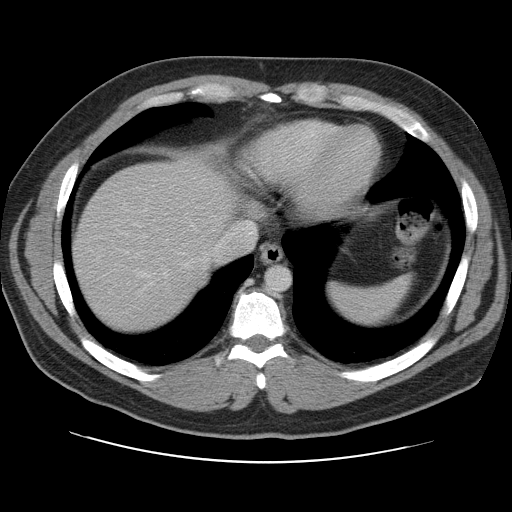
Contrast-enhanced abdominal CT, one axial slice. Position 96 of 109 along the scan axis. 120 kVp. Intravenous contrast given. Soft-tissue window (W 400 / L 40 HU). 512 × 512 image matrix, field of view 402 × 402 mm. Male patient, age 35 years. Case-level facts recorded for this patient, not image findings: diagnosis: colorectal cancer liver metastases, imaged before liver resection; multiple liver metastases: yes; largest metastasis: 2.8 cm; disease in both lobes: yes.
Annotated regions visible in this slice (manually delineated by an expert):
- hepatic veins: box from (x=136, y=222) to (x=256, y=278) px
- liver: (x=72, y=160)–(x=236, y=332)
- planned liver remnant (the part of the liver to remain after resection): (x=72, y=159)–(x=236, y=332)